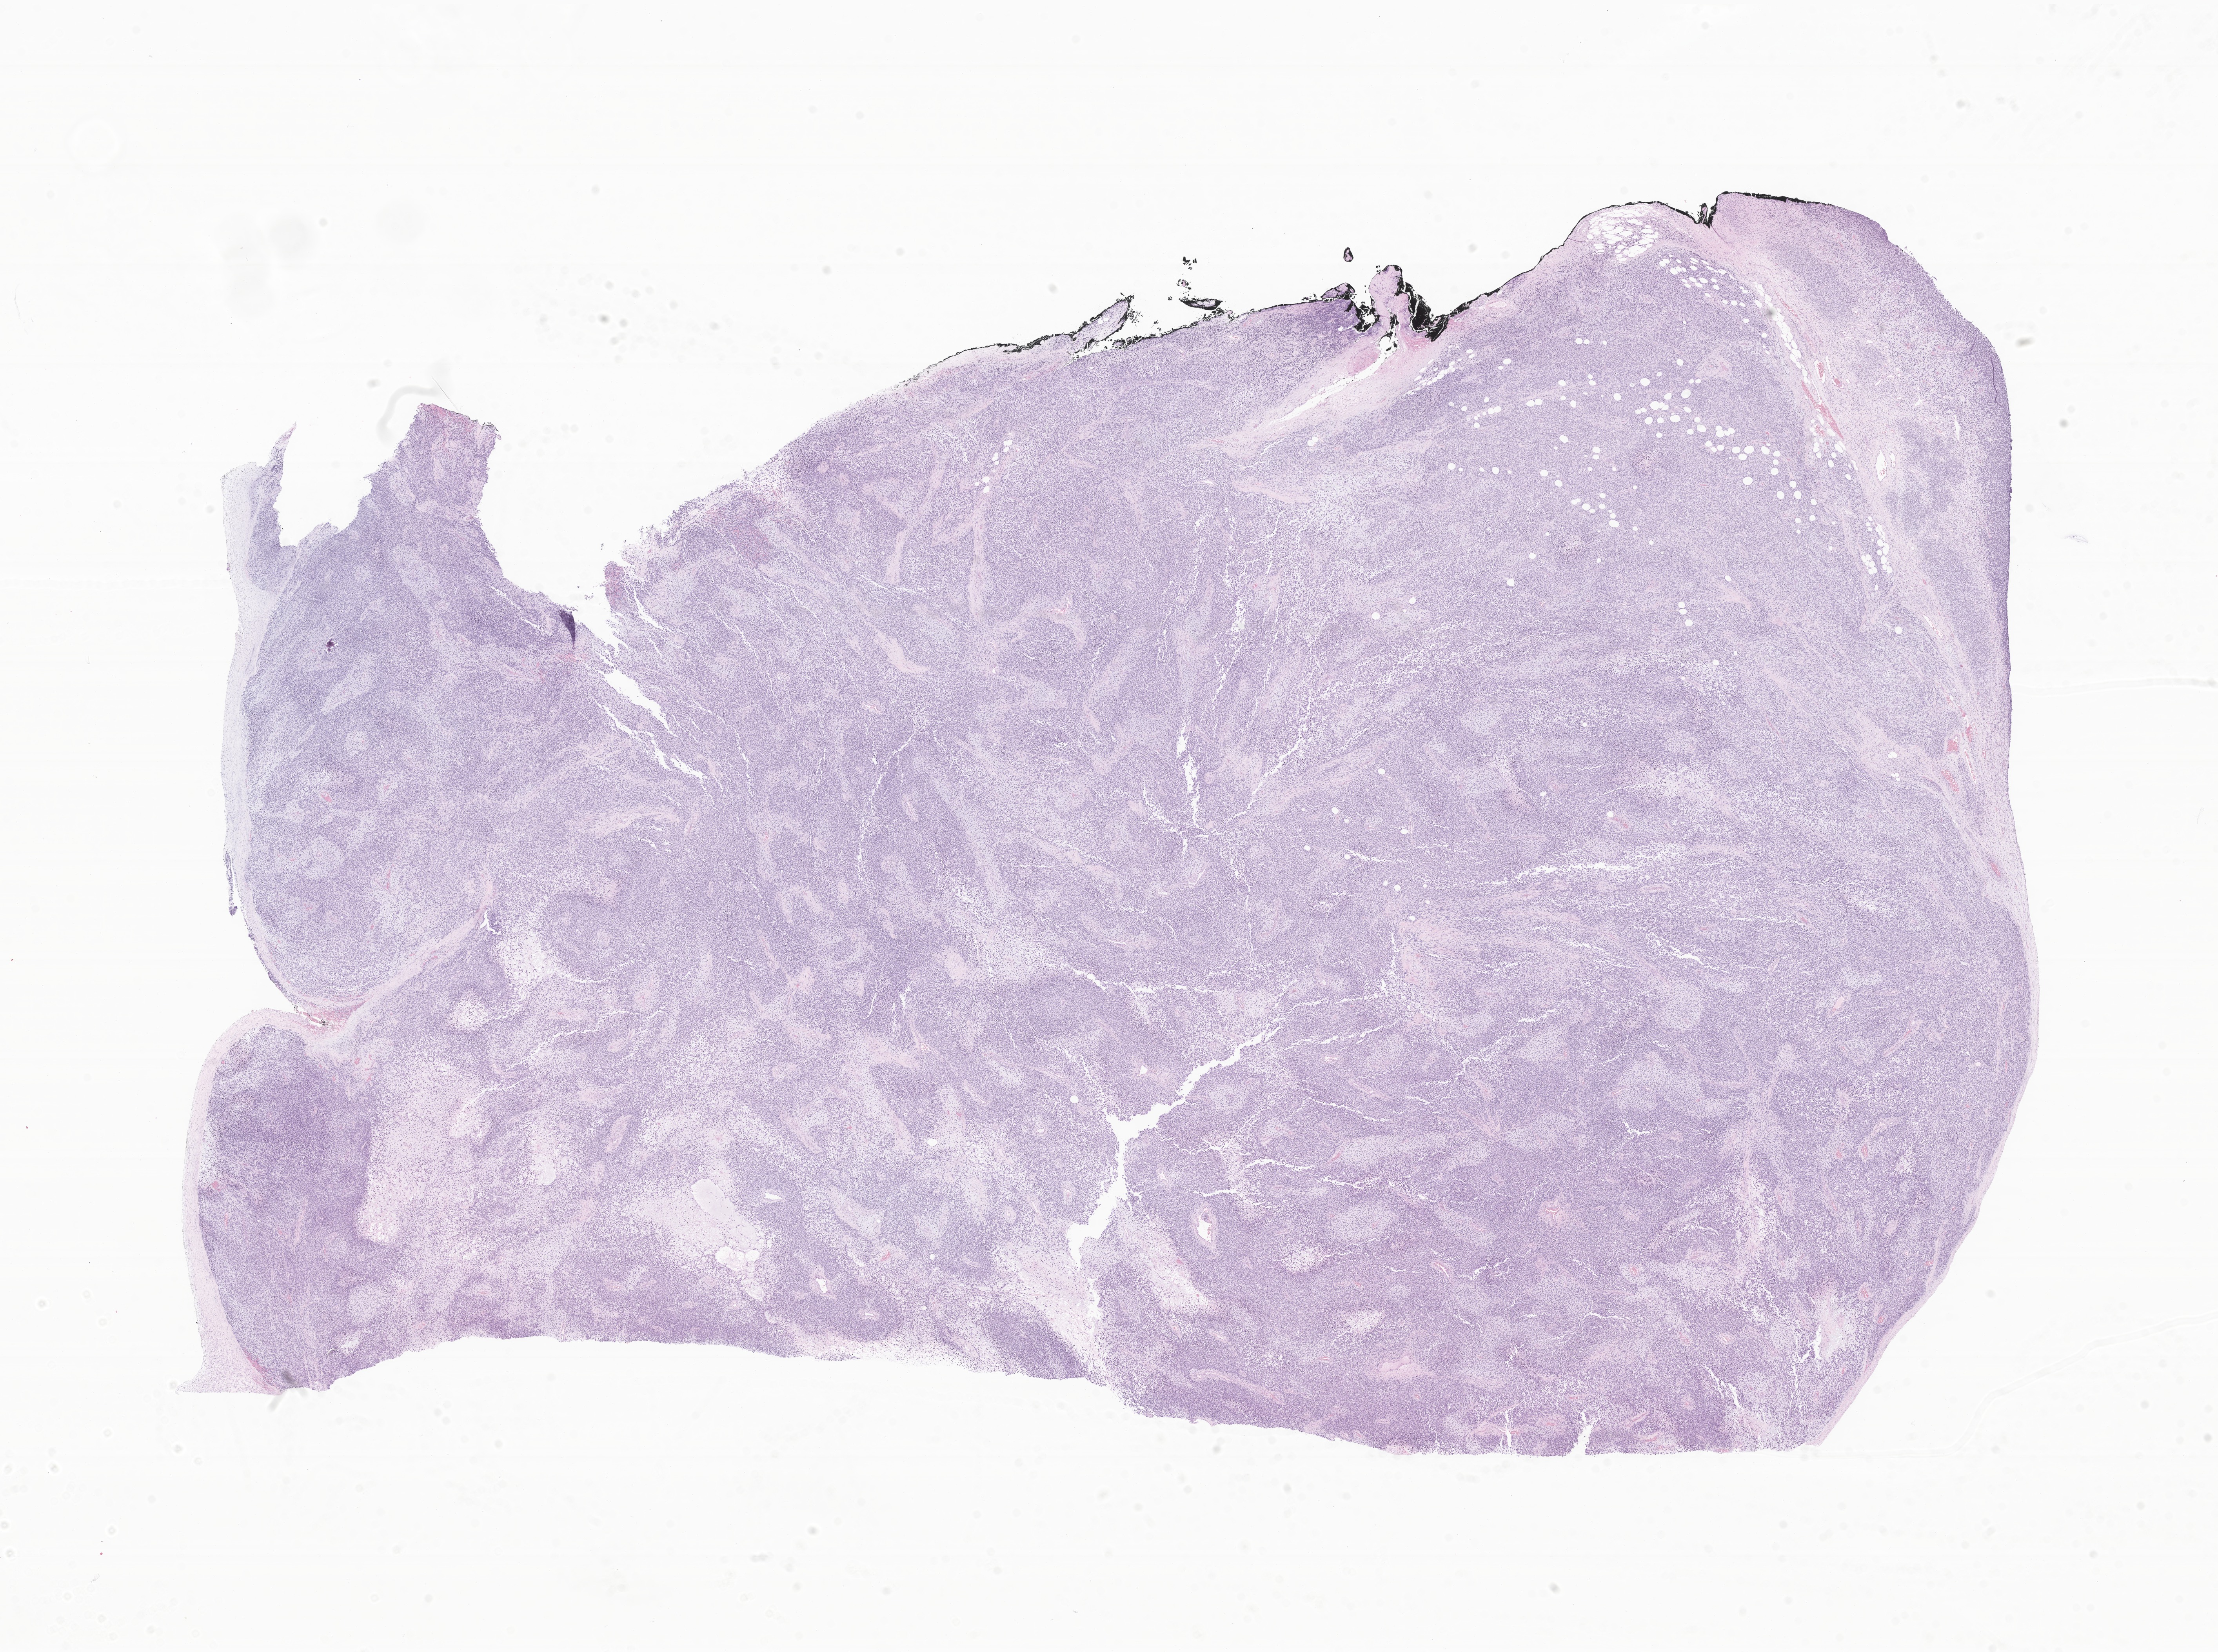
Haematoxylin and eosin whole-slide image of tumor tissue from the pelvis — shown as a low-resolution overview of the whole scanned area (about 23.8 x 17.8 mm). Formalin-fixed, paraffin-embedded (FFPE) tissue. Patient female; age 78 months (6 years 6 months).
Diagnosis (ICD-O-3 morphology term): Embryonal rhabdomyosarcoma, NOS.